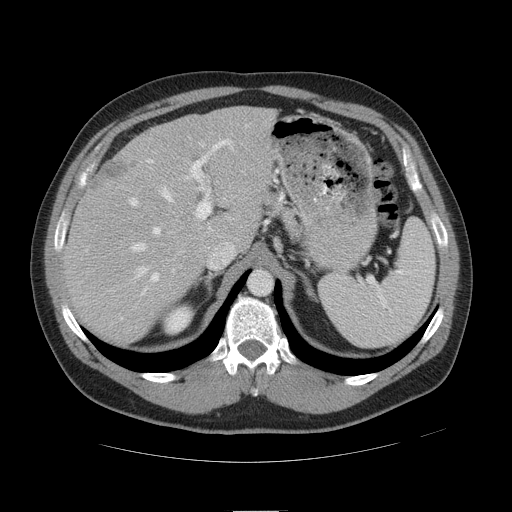
Contrast-enhanced abdominal CT, one axial slice; position 32 of 49 along the scan axis; reconstruction kernel STANDARD; 120 kVp; intravenous contrast given; soft-tissue window (W 400 / L 40 HU); 512 × 512 image matrix, field of view 425 × 425 mm. Male patient, age 52 years. From the clinical record (not read from this slice): diagnosis: colorectal cancer liver metastases, imaged before liver resection; multiple liver metastases: yes; largest metastasis: 5.1 cm; chemotherapy before resection: yes.
Structures marked on this image (manually delineated by an expert):
- hepatic veins: box from (x=131, y=143) to (x=205, y=278) px
- liver: (x=68, y=109)–(x=271, y=343)
- planned liver remnant (the part of the liver to remain after resection): (x=136, y=108)–(x=270, y=243)
- portal vein (with intrahepatic branches): (x=128, y=139)–(x=232, y=283)
- liver metastasis: (x=102, y=162)–(x=130, y=181)